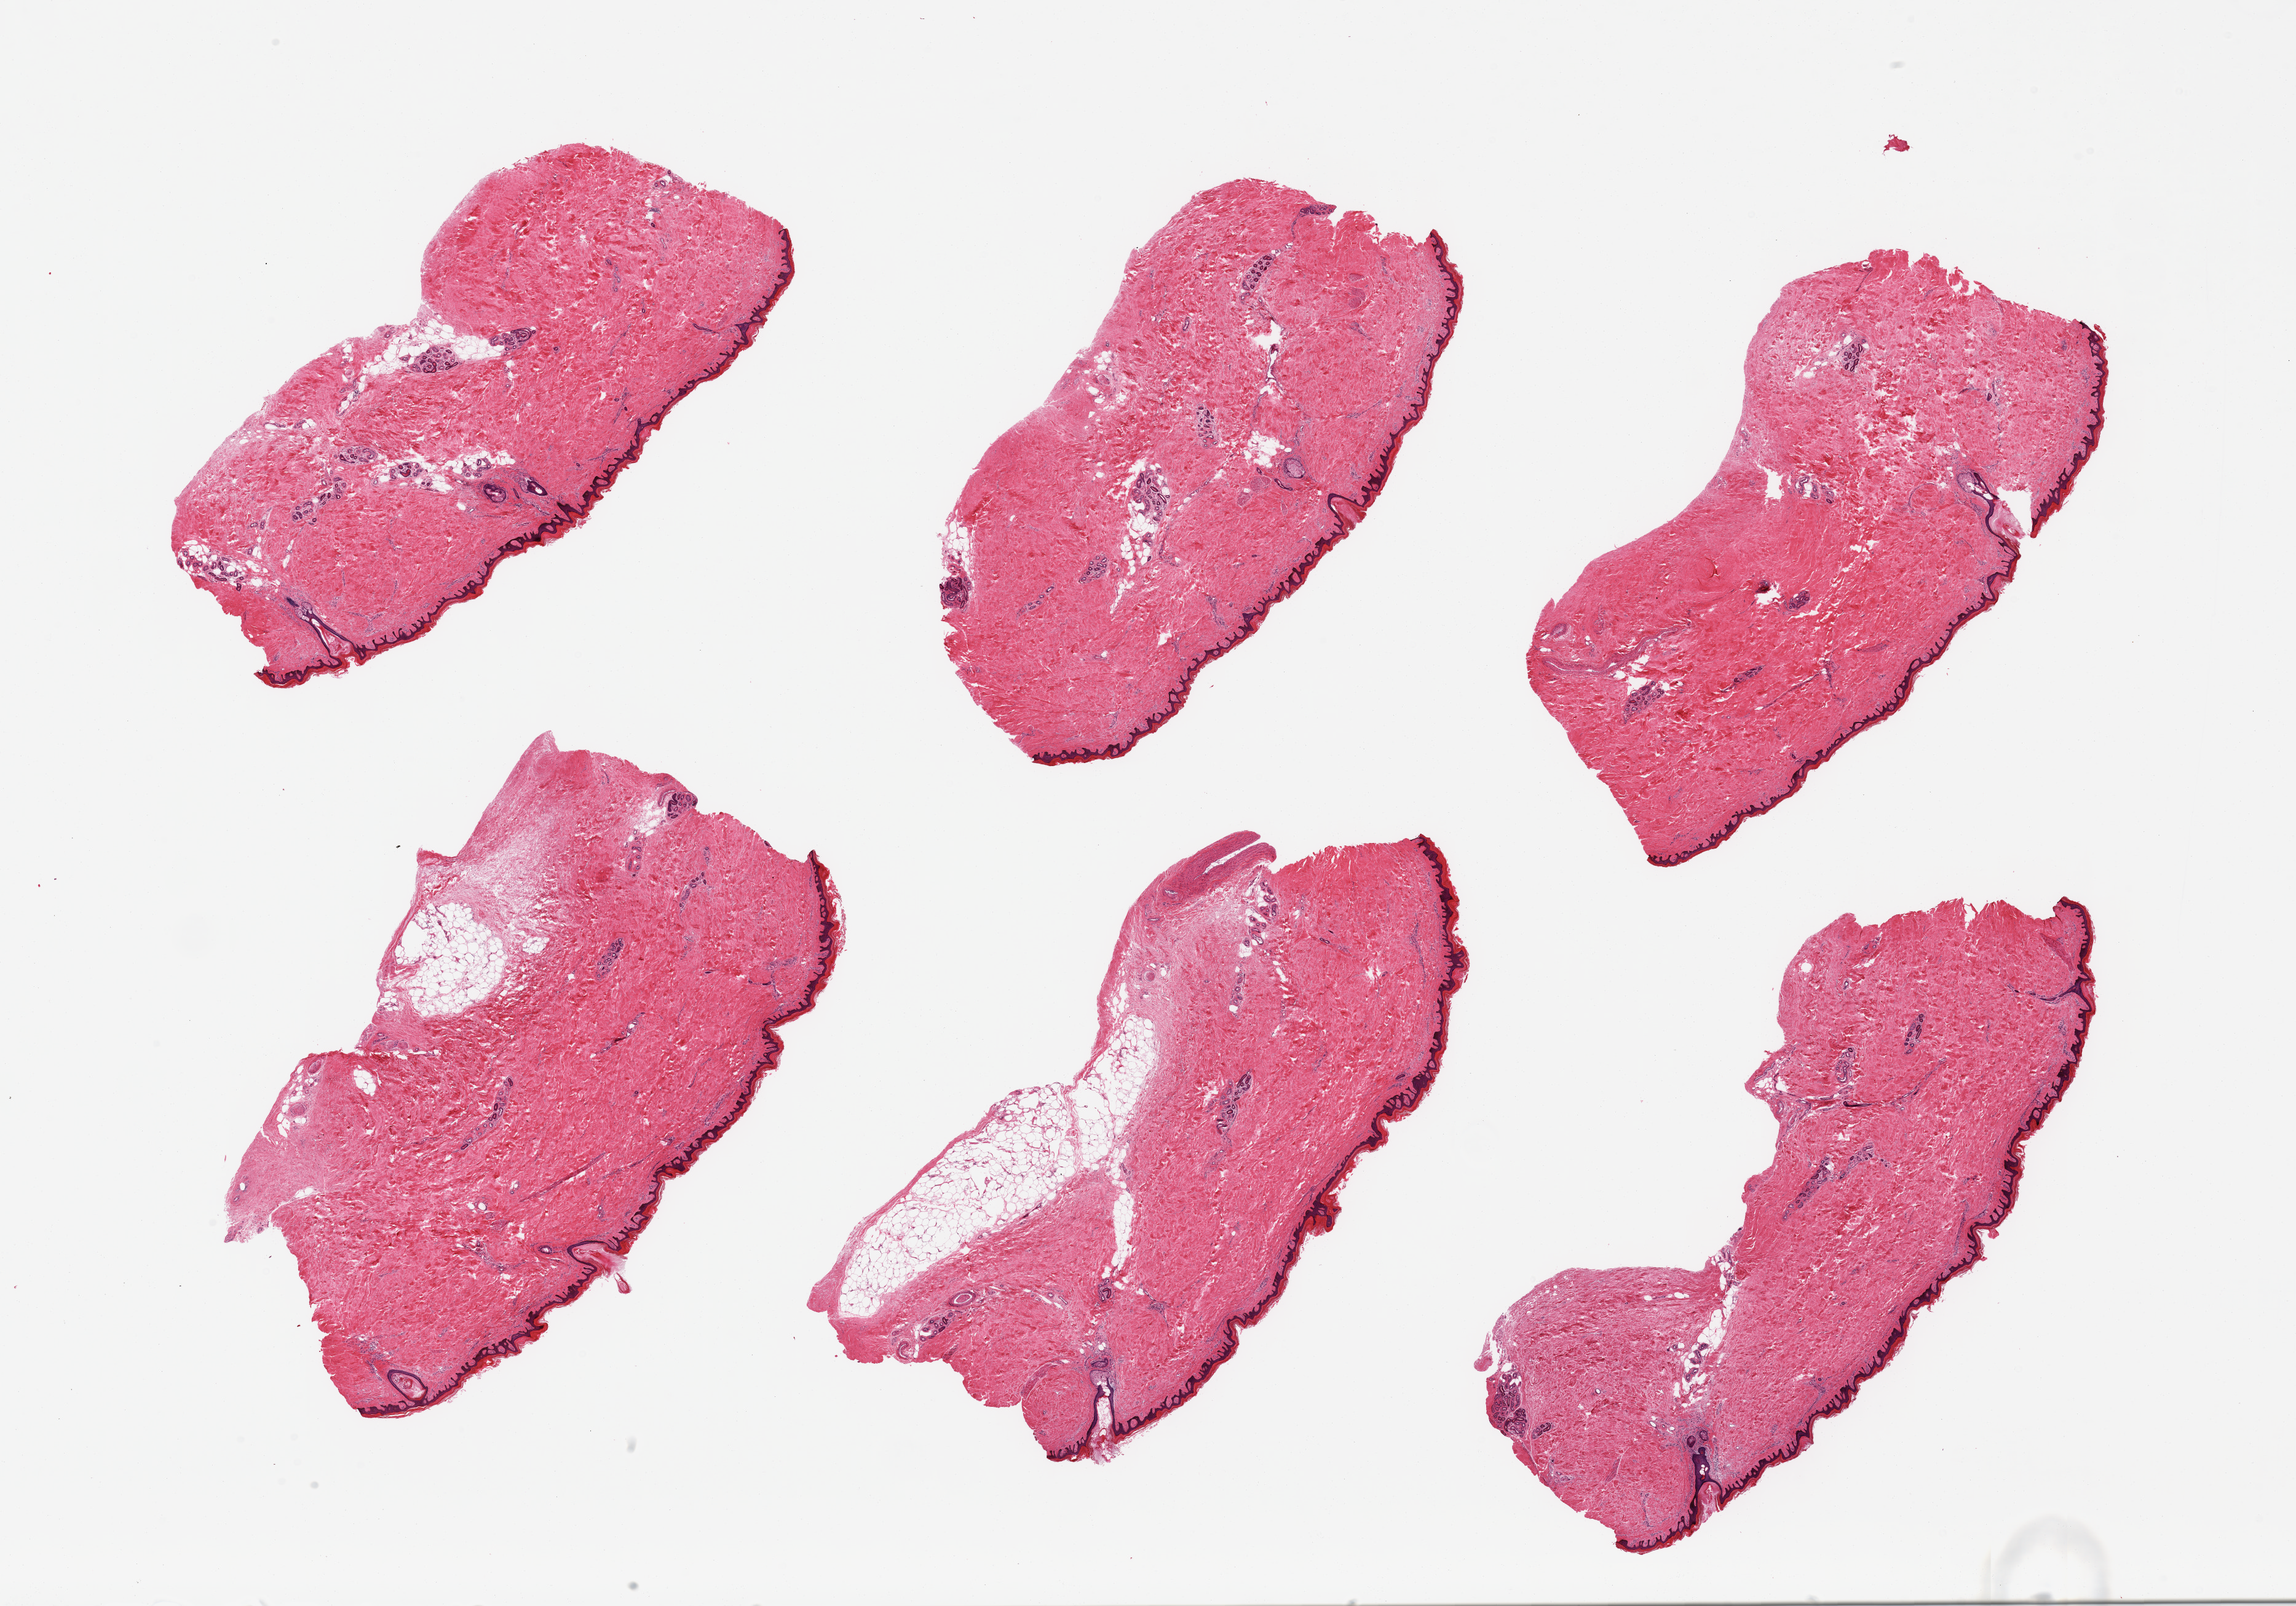
Whole-slide image, hematoxylin and eosin (H&E) stain, brightfield — shown as a low-resolution overview of the whole scanned area (about 29.5 x 20.7 mm, slide scanned at 20x). PAXgene-fixed, paraffin-embedded tissue. Section of skin of lower leg (target tissue). Donor tissue sample. Donor sex: male.
* reviewer comment on this tissue sample: 6 pieces; periadnexal fat and 5% and 15% external fat